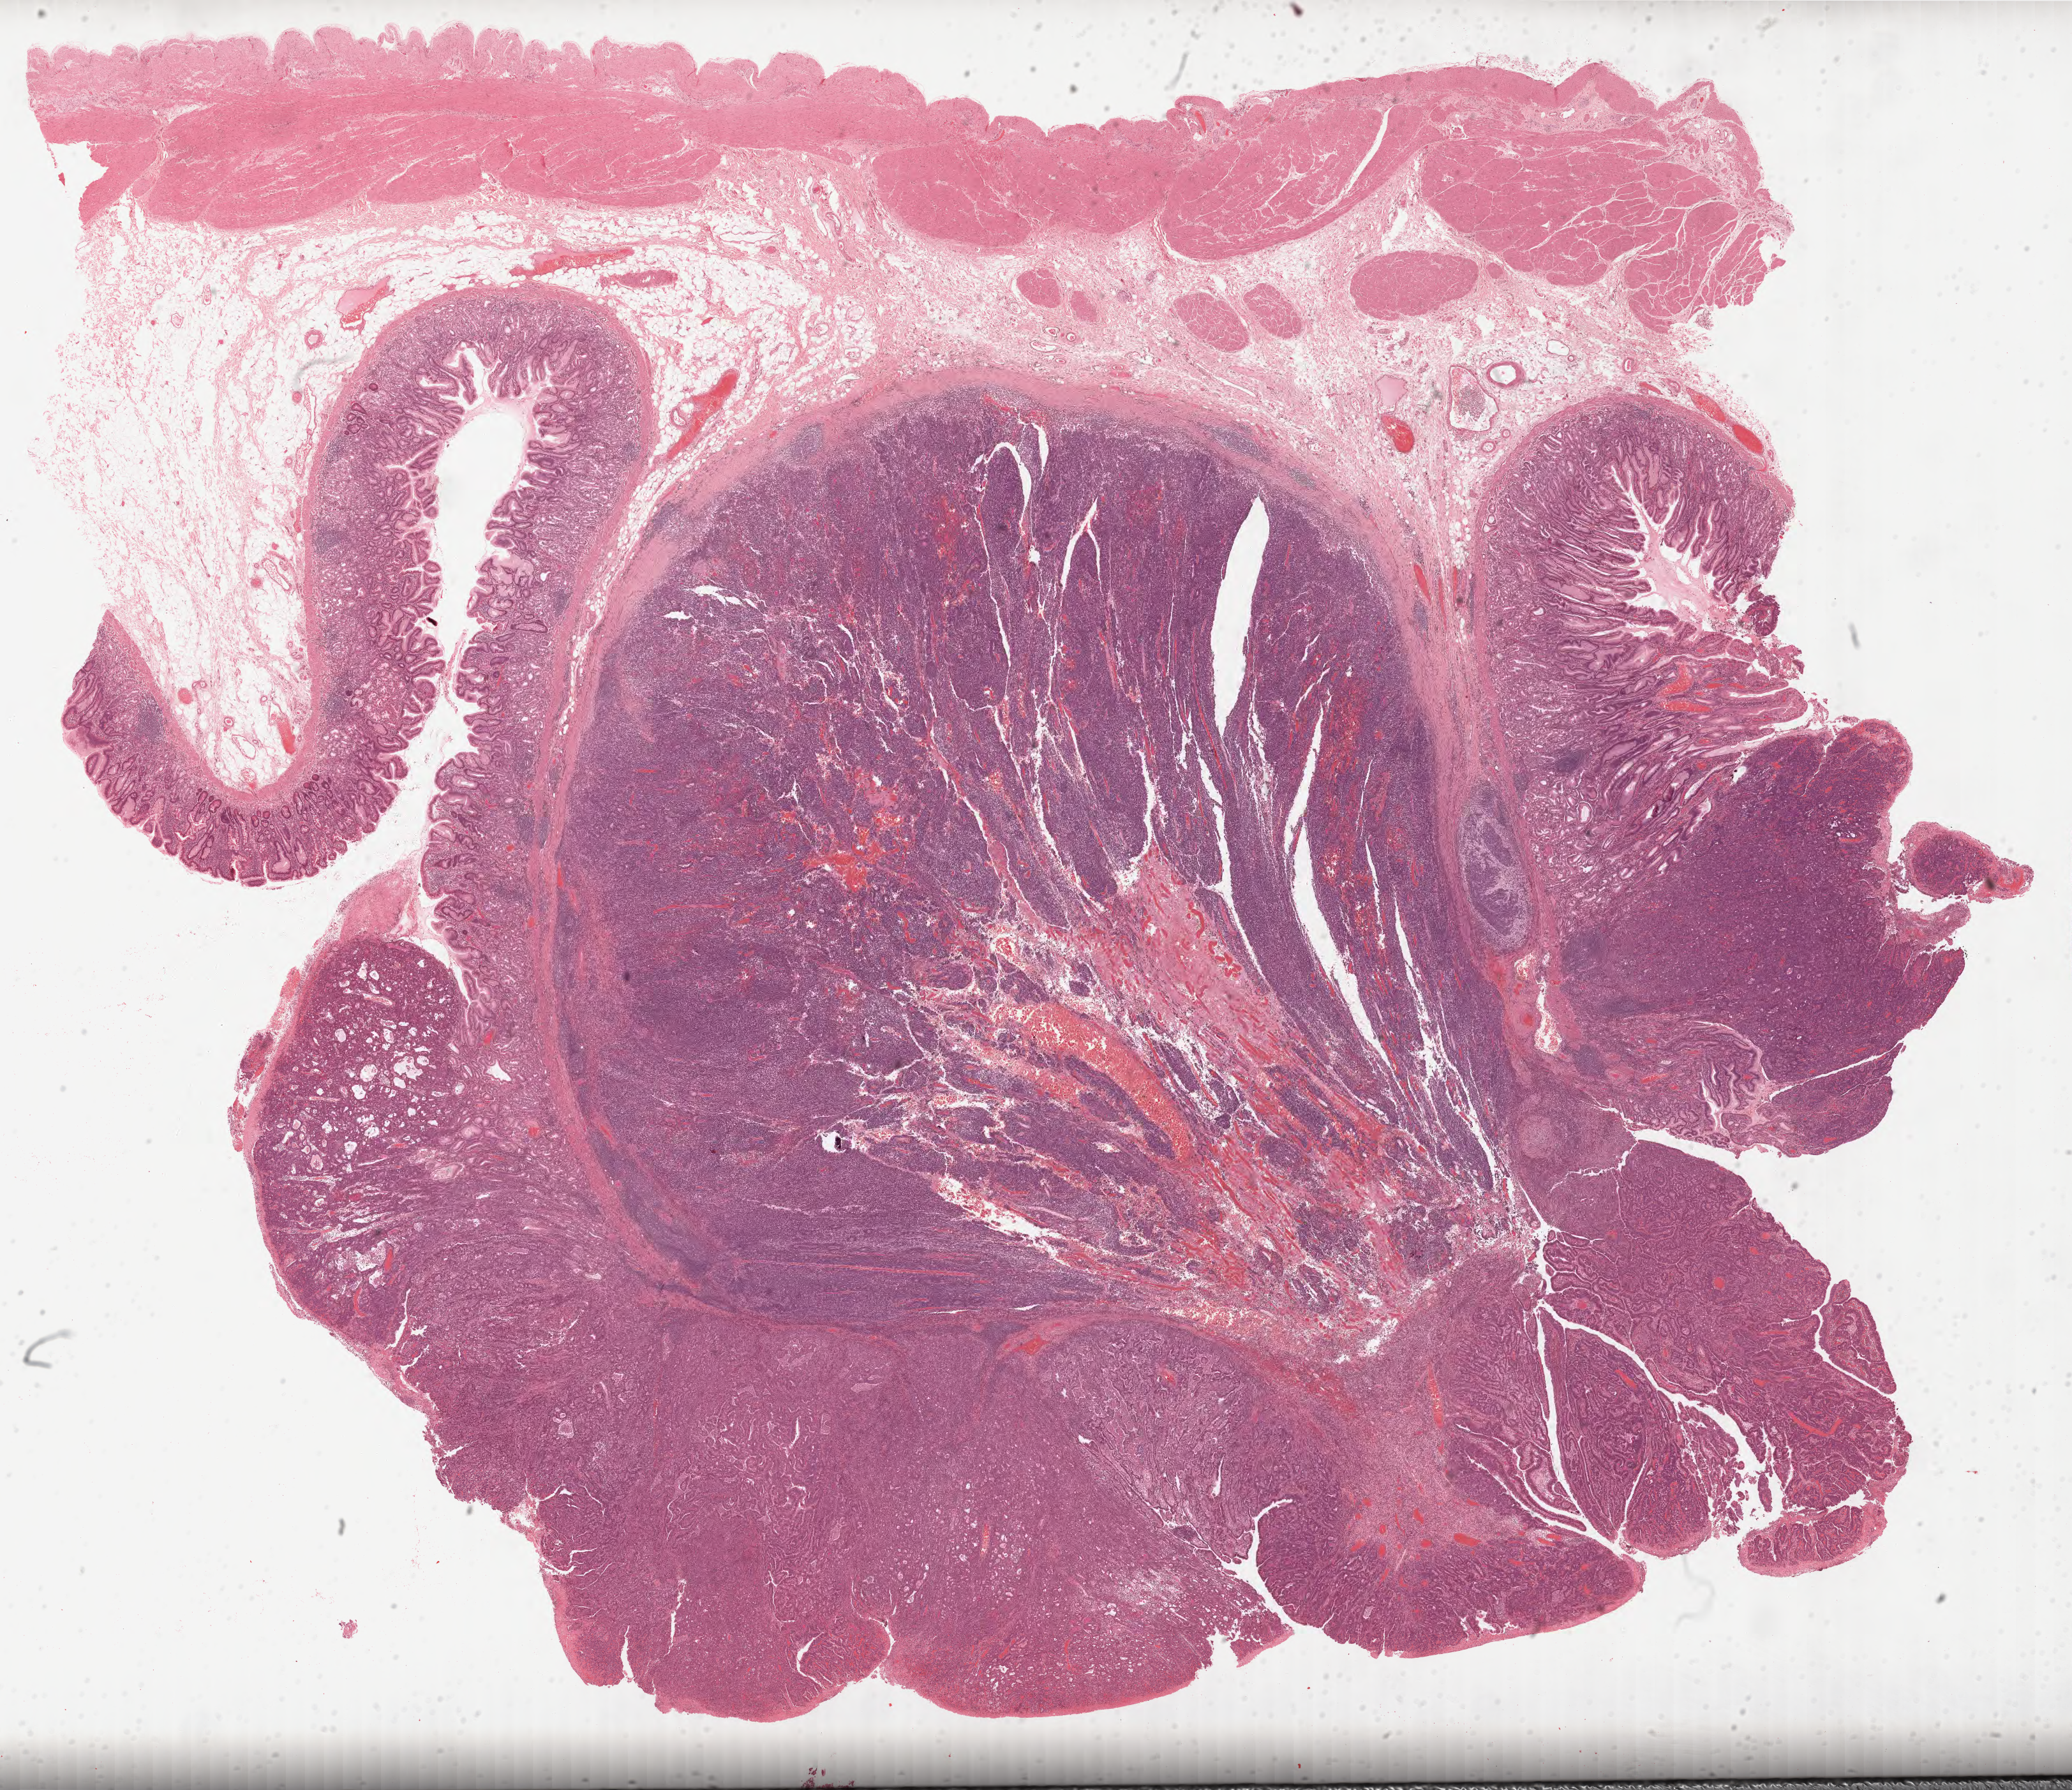
Digitized H&E tissue section (whole slide) — shown as a low-resolution overview of the whole scanned area (about 26.2 x 22.6 mm, acquisition: 40x scan), formalin-fixed paraffin-embedded (FFPE) diagnostic section, stomach, primary tumour sample. Female patient; age at initial diagnosis 54 years. Histologic grade: G3 (poorly differentiated).
- histologic diagnosis: Adenocarcinoma, intestinal type
- AJCC pathologic stage: IB (6th edition)
- lymph nodes positive (case pathology): 1 of 30 examined